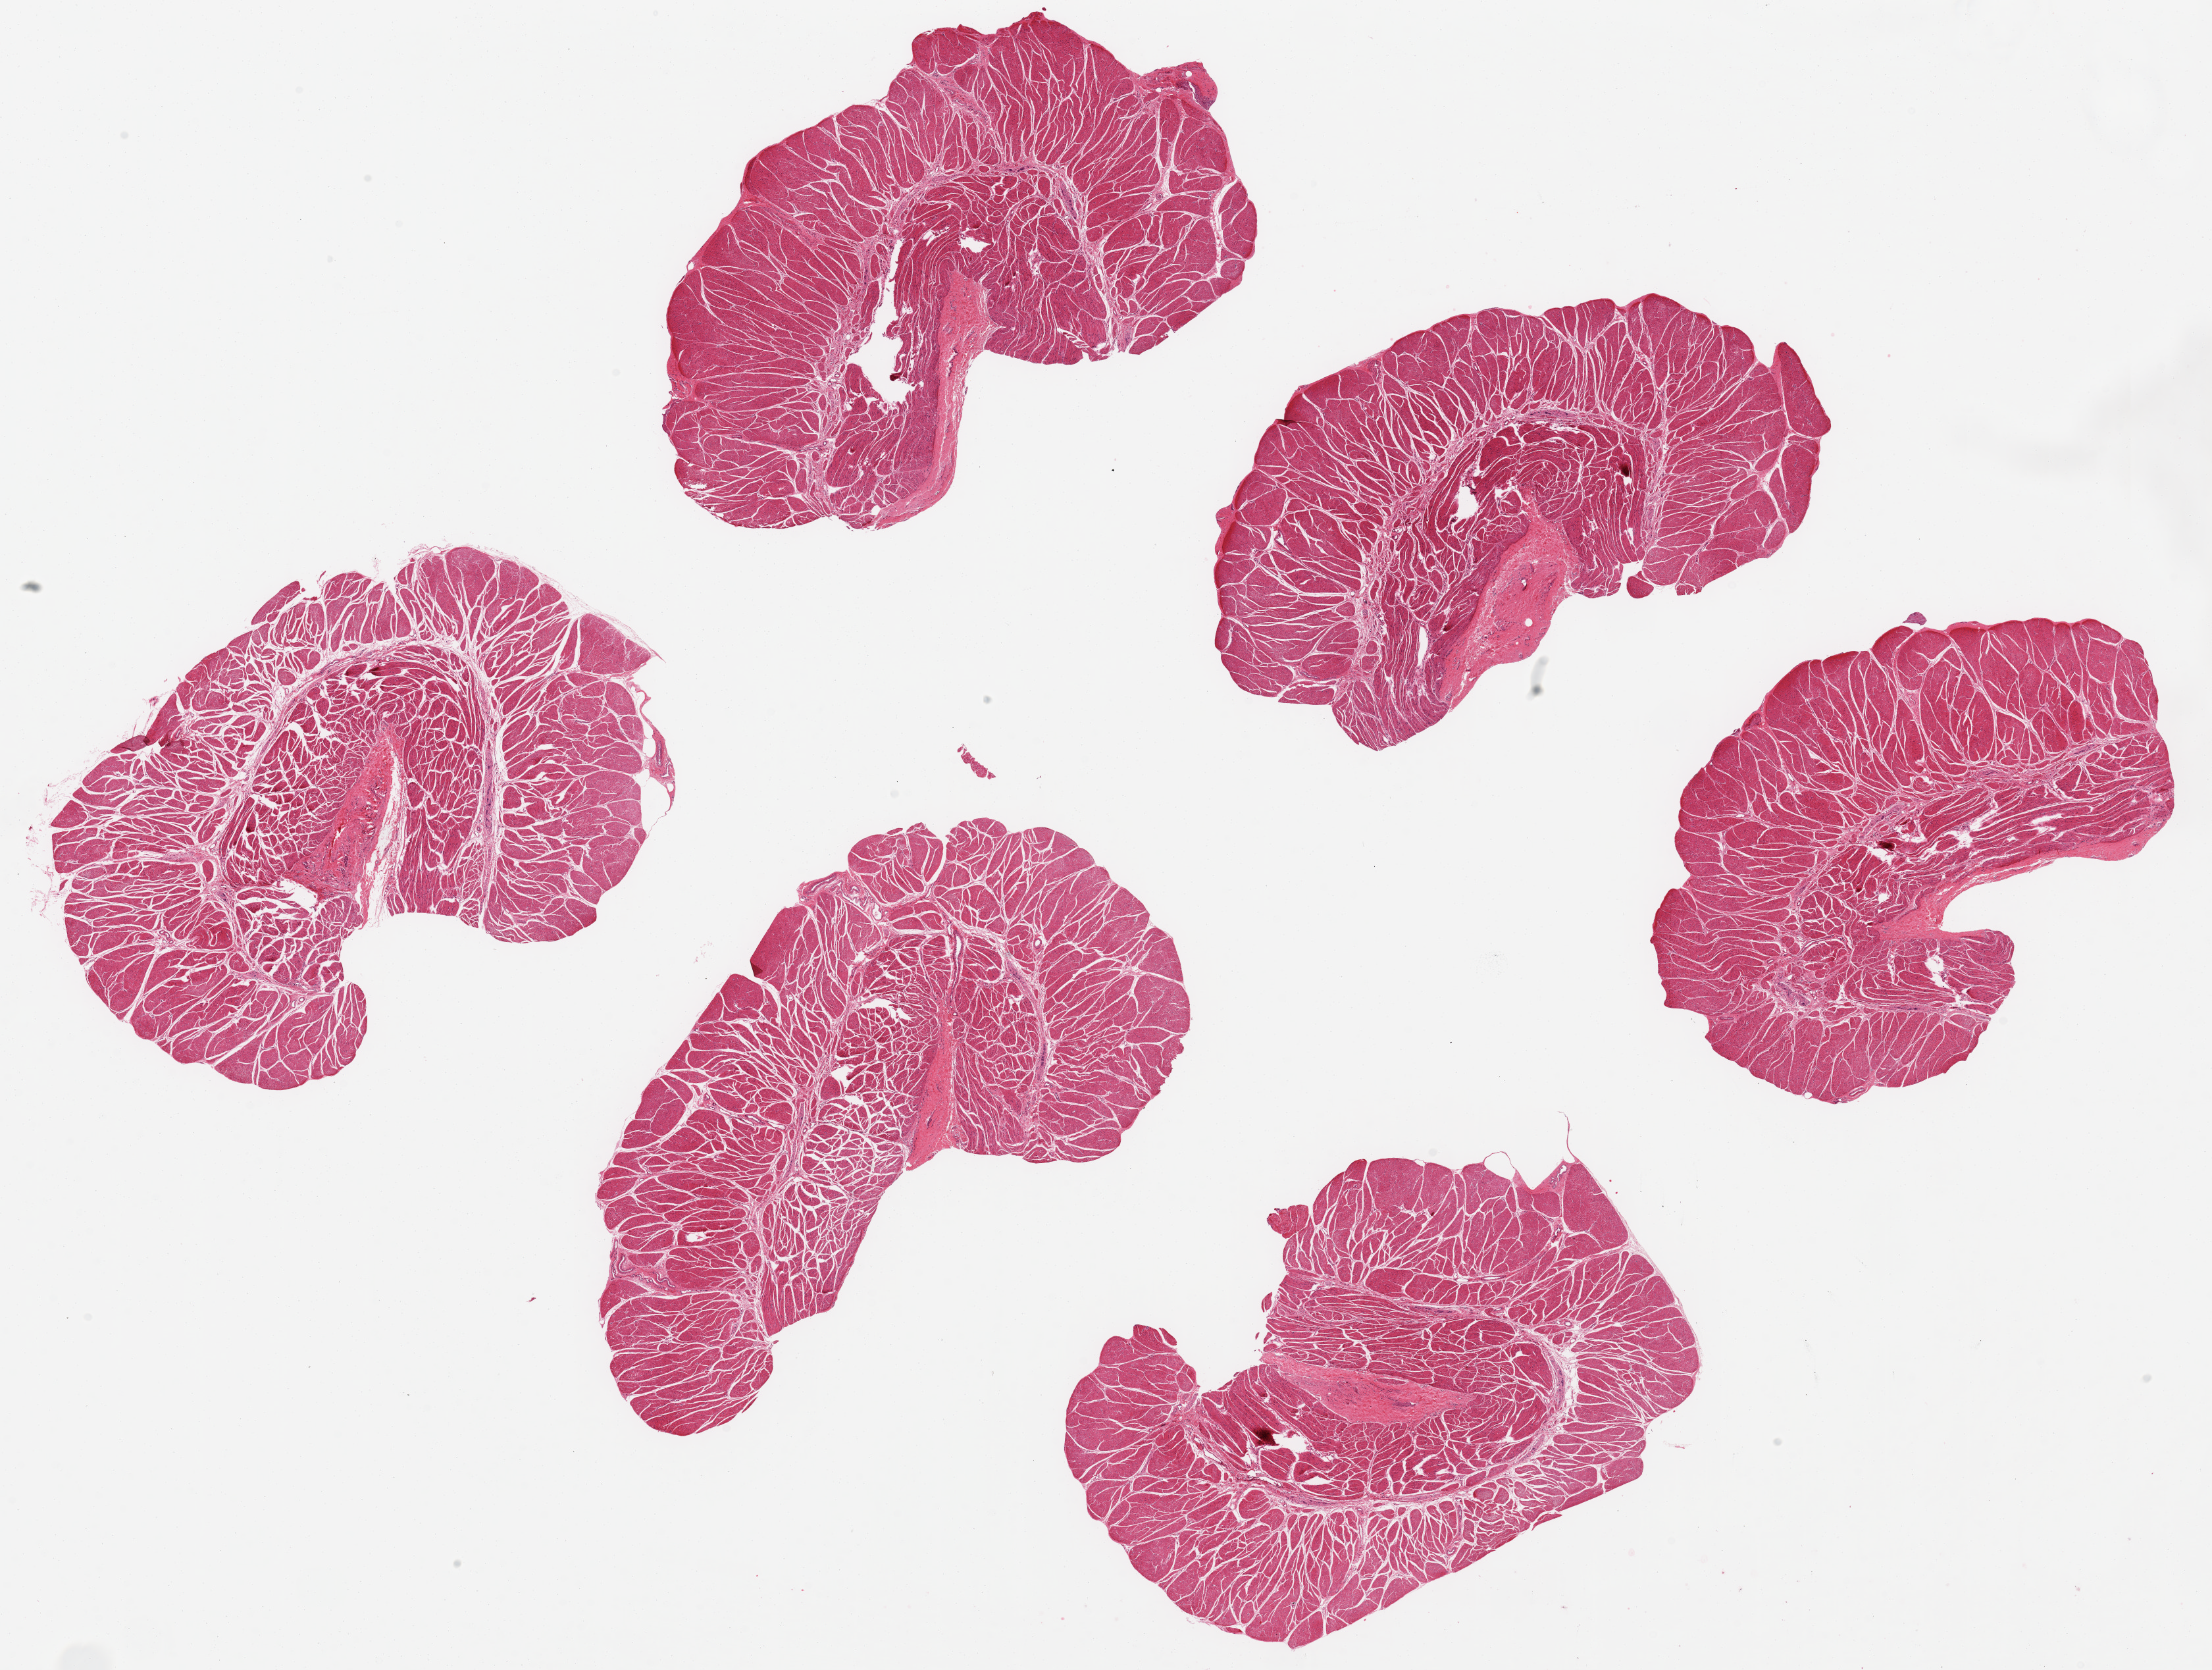
Whole-slide image, hematoxylin and eosin (H&E) stain, low-resolution overview of the scanned area, about 26.6 x 20.1 mm; PAXgene-fixed paraffin-embedded (PFPE) section; target tissue: esophageal muscle; tissue donor sample.
- review note (as recorded): 6 pieces up to 8.5x4.9 mm; good muscle layer